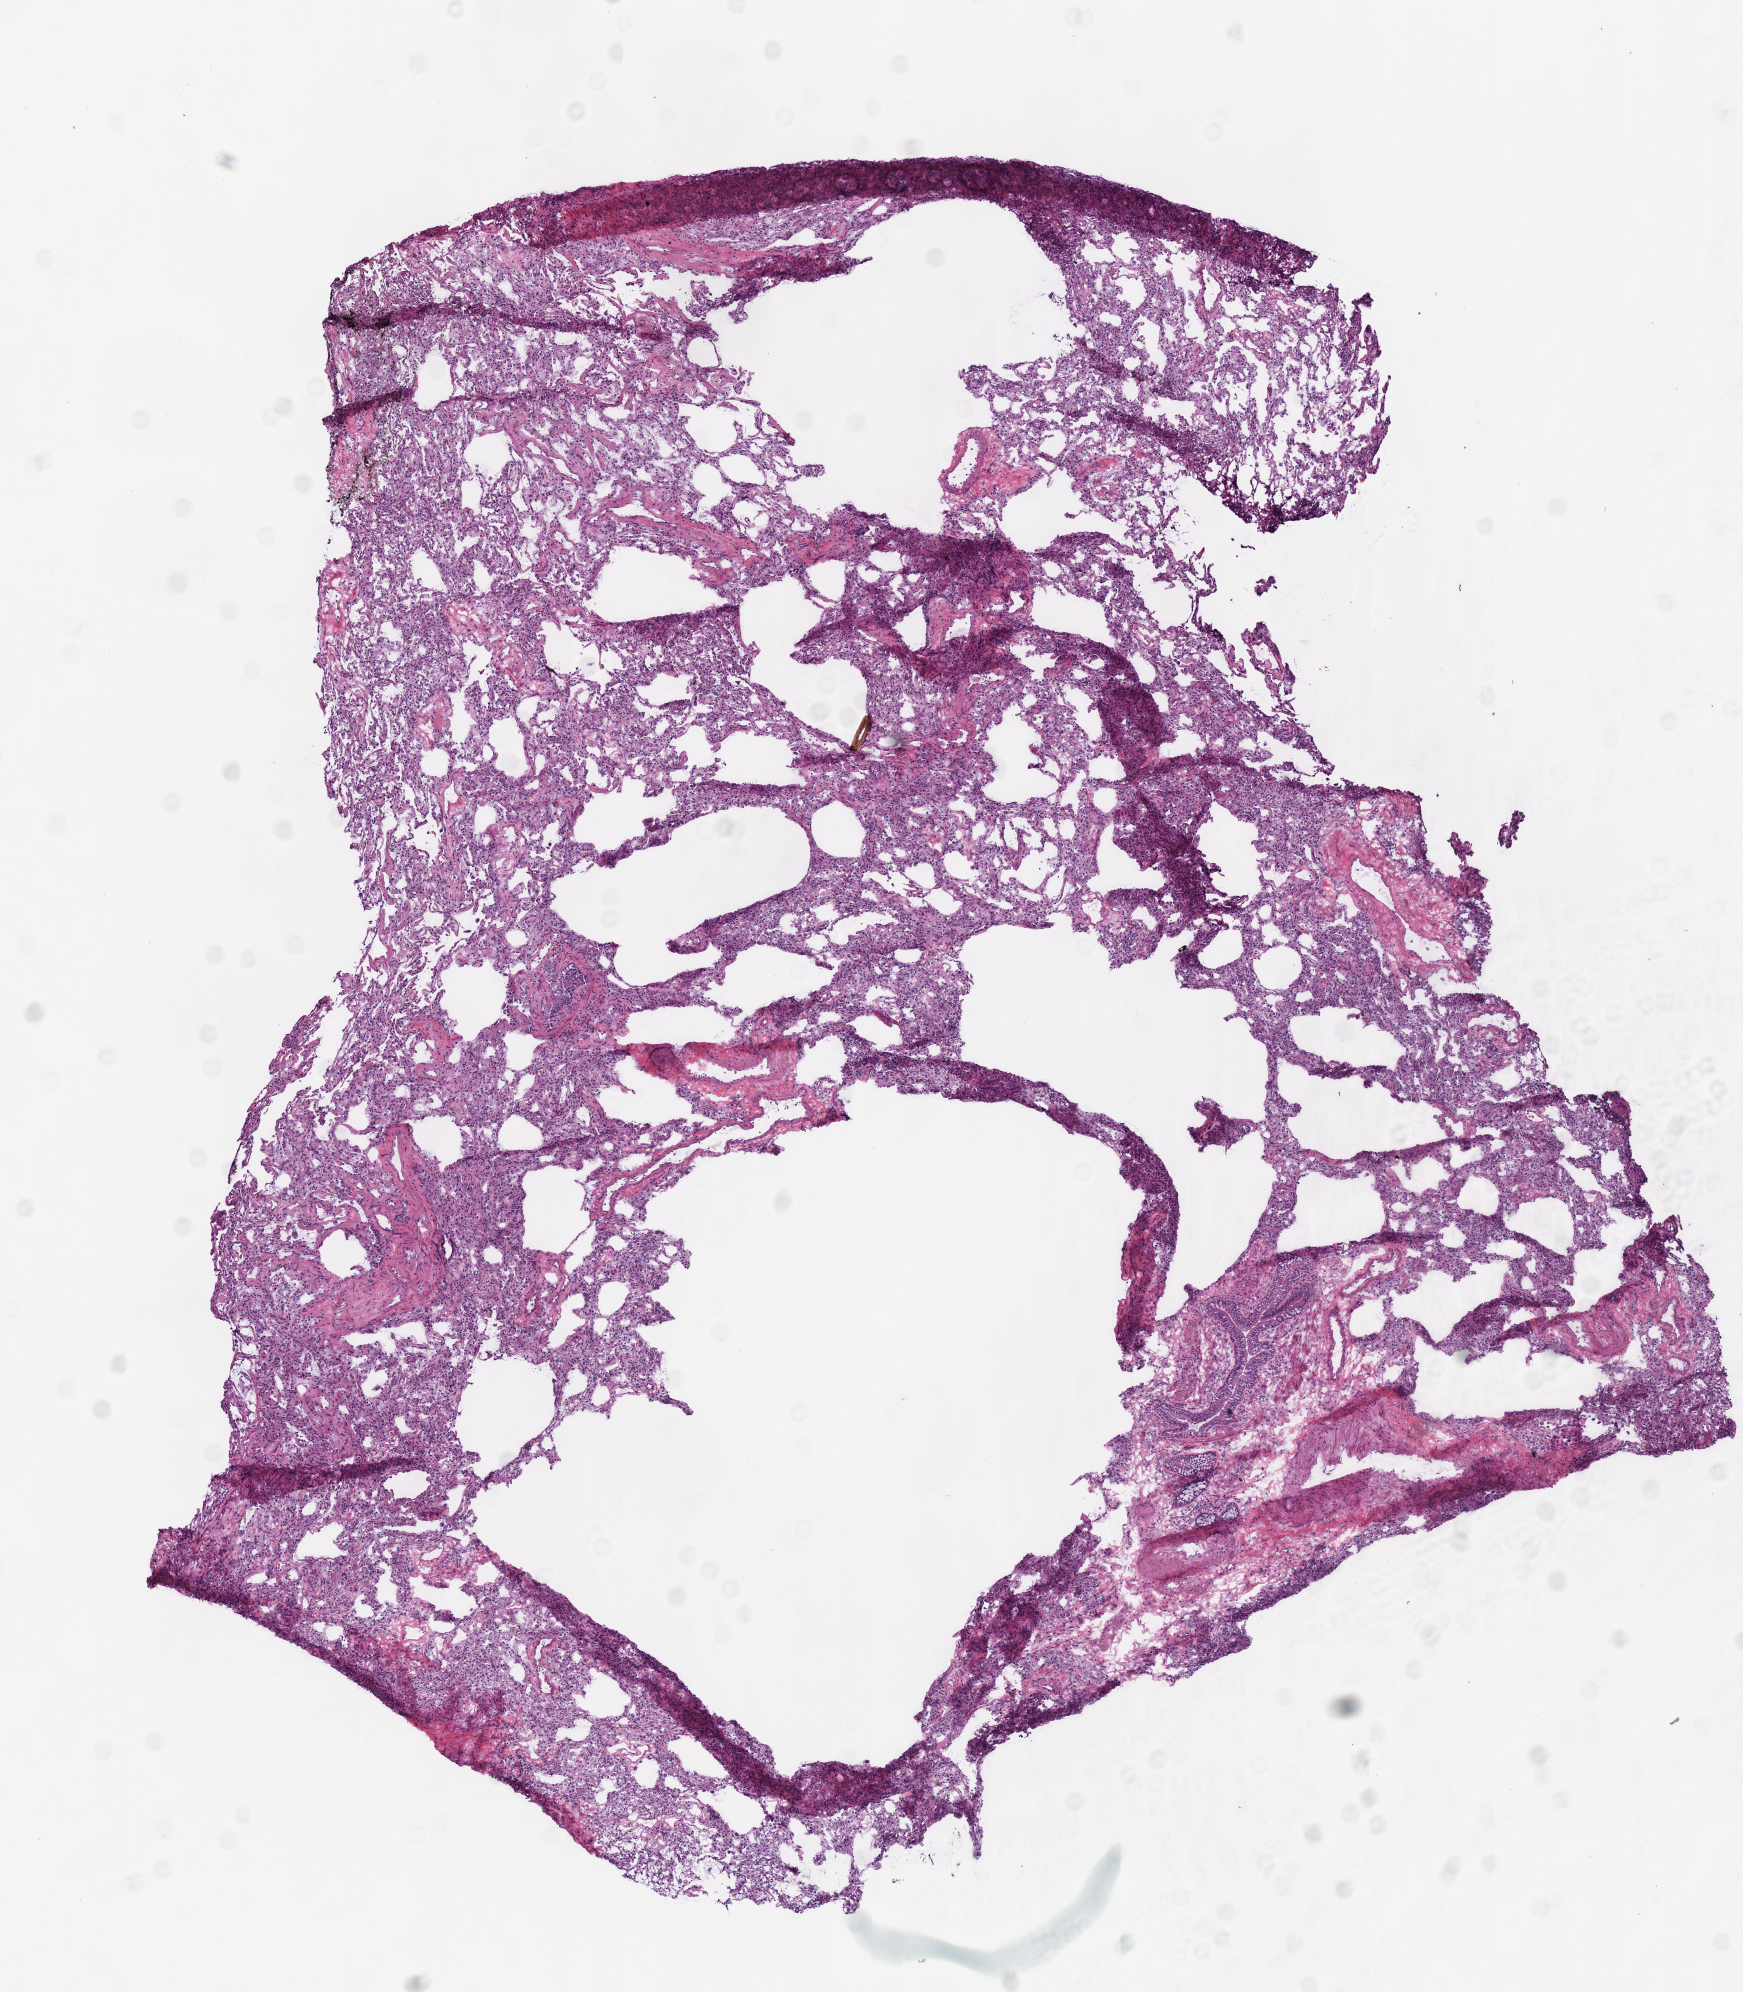
Whole-slide histology image, H&E — low-resolution overview of the scanned area, about 6.9 x 7.8 mm; frozen section from the top of the tissue portion; lung, solid tissue normal (non-tumour tissue) sample. Patient: female, age at initial diagnosis 72 years.
This section: solid tissue normal (non-tumour) sample from the same patient. Patient diagnosis: Adenocarcinoma, NOS (lower lobe, lung).